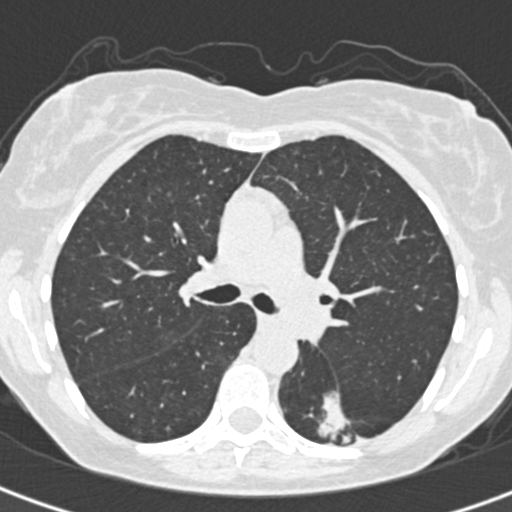
Low-dose screening chest CT, one axial slice. Slice 209 of 328 in the series (ordered by position). Reconstruction kernel B30f. Lung window (W 1500 / L -600 HU). 1 mm slice thickness. 512 × 512 image matrix, field of view 284 × 284 mm.
Structures marked on this image (outlined manually by an expert reader):
- lesion 1 (tumor, lower lobe of left lung): bounding box <319,393,350,443> (left, top, right, bottom; pixels)